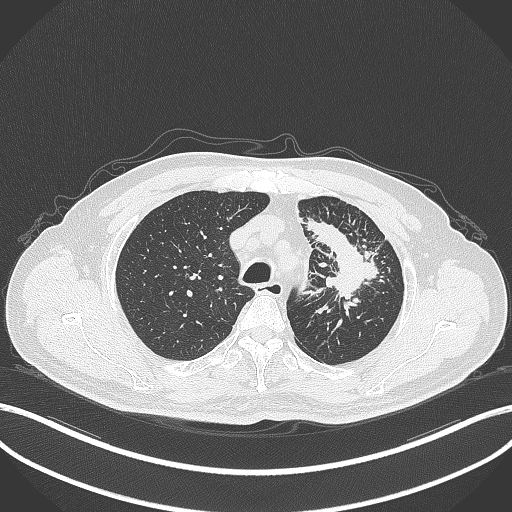
Chest CT, one axial slice; slice 278 of 386 in the series (ordered by position); reconstruction kernel B70f; 120 kVp; lung window (W 1500 / L -600 HU); 1 mm slice thickness; 512 × 512 image matrix. Male patient, age 69 years. From the clinical record (not read from this slice): clinical TNM (as recorded): T2a N2 M0; histopathological grade: G2-3.
Outlined on this slice (rectangle marked by the reading radiologist):
- lung tumour (recorded histology: adenocarcinoma): bounding box <304,216,385,300> (left, top, right, bottom; pixels)